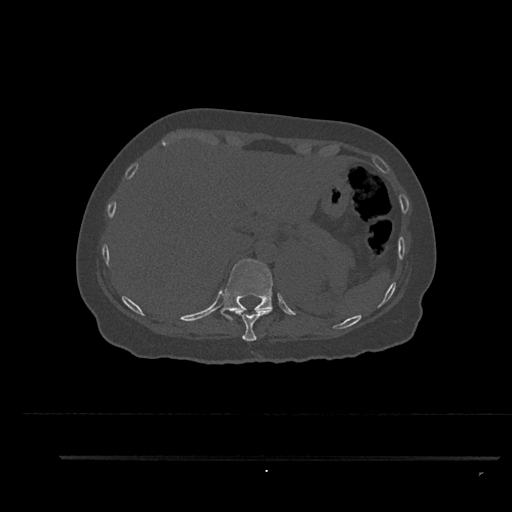
CT including the spine, one axial slice; position 336 of 797 along the scan axis; reconstruction kernel Br40s/3; bone window (W 1800 / L 400 HU); 512 × 512 image matrix, field of view 408 × 408 mm. Patient: female, 44 years. Case-level facts recorded for this patient, not image findings: primary cancer: renal; vertebrae with lytic lesions (as recorded): L1.
Annotated regions visible in this slice (semi-automatic segmentation, software-assisted and operator-edited):
- T10 vertebra: bounding box <227,308,272,341> (left, top, right, bottom; pixels)
- T11 vertebra: <220,259,273,321>